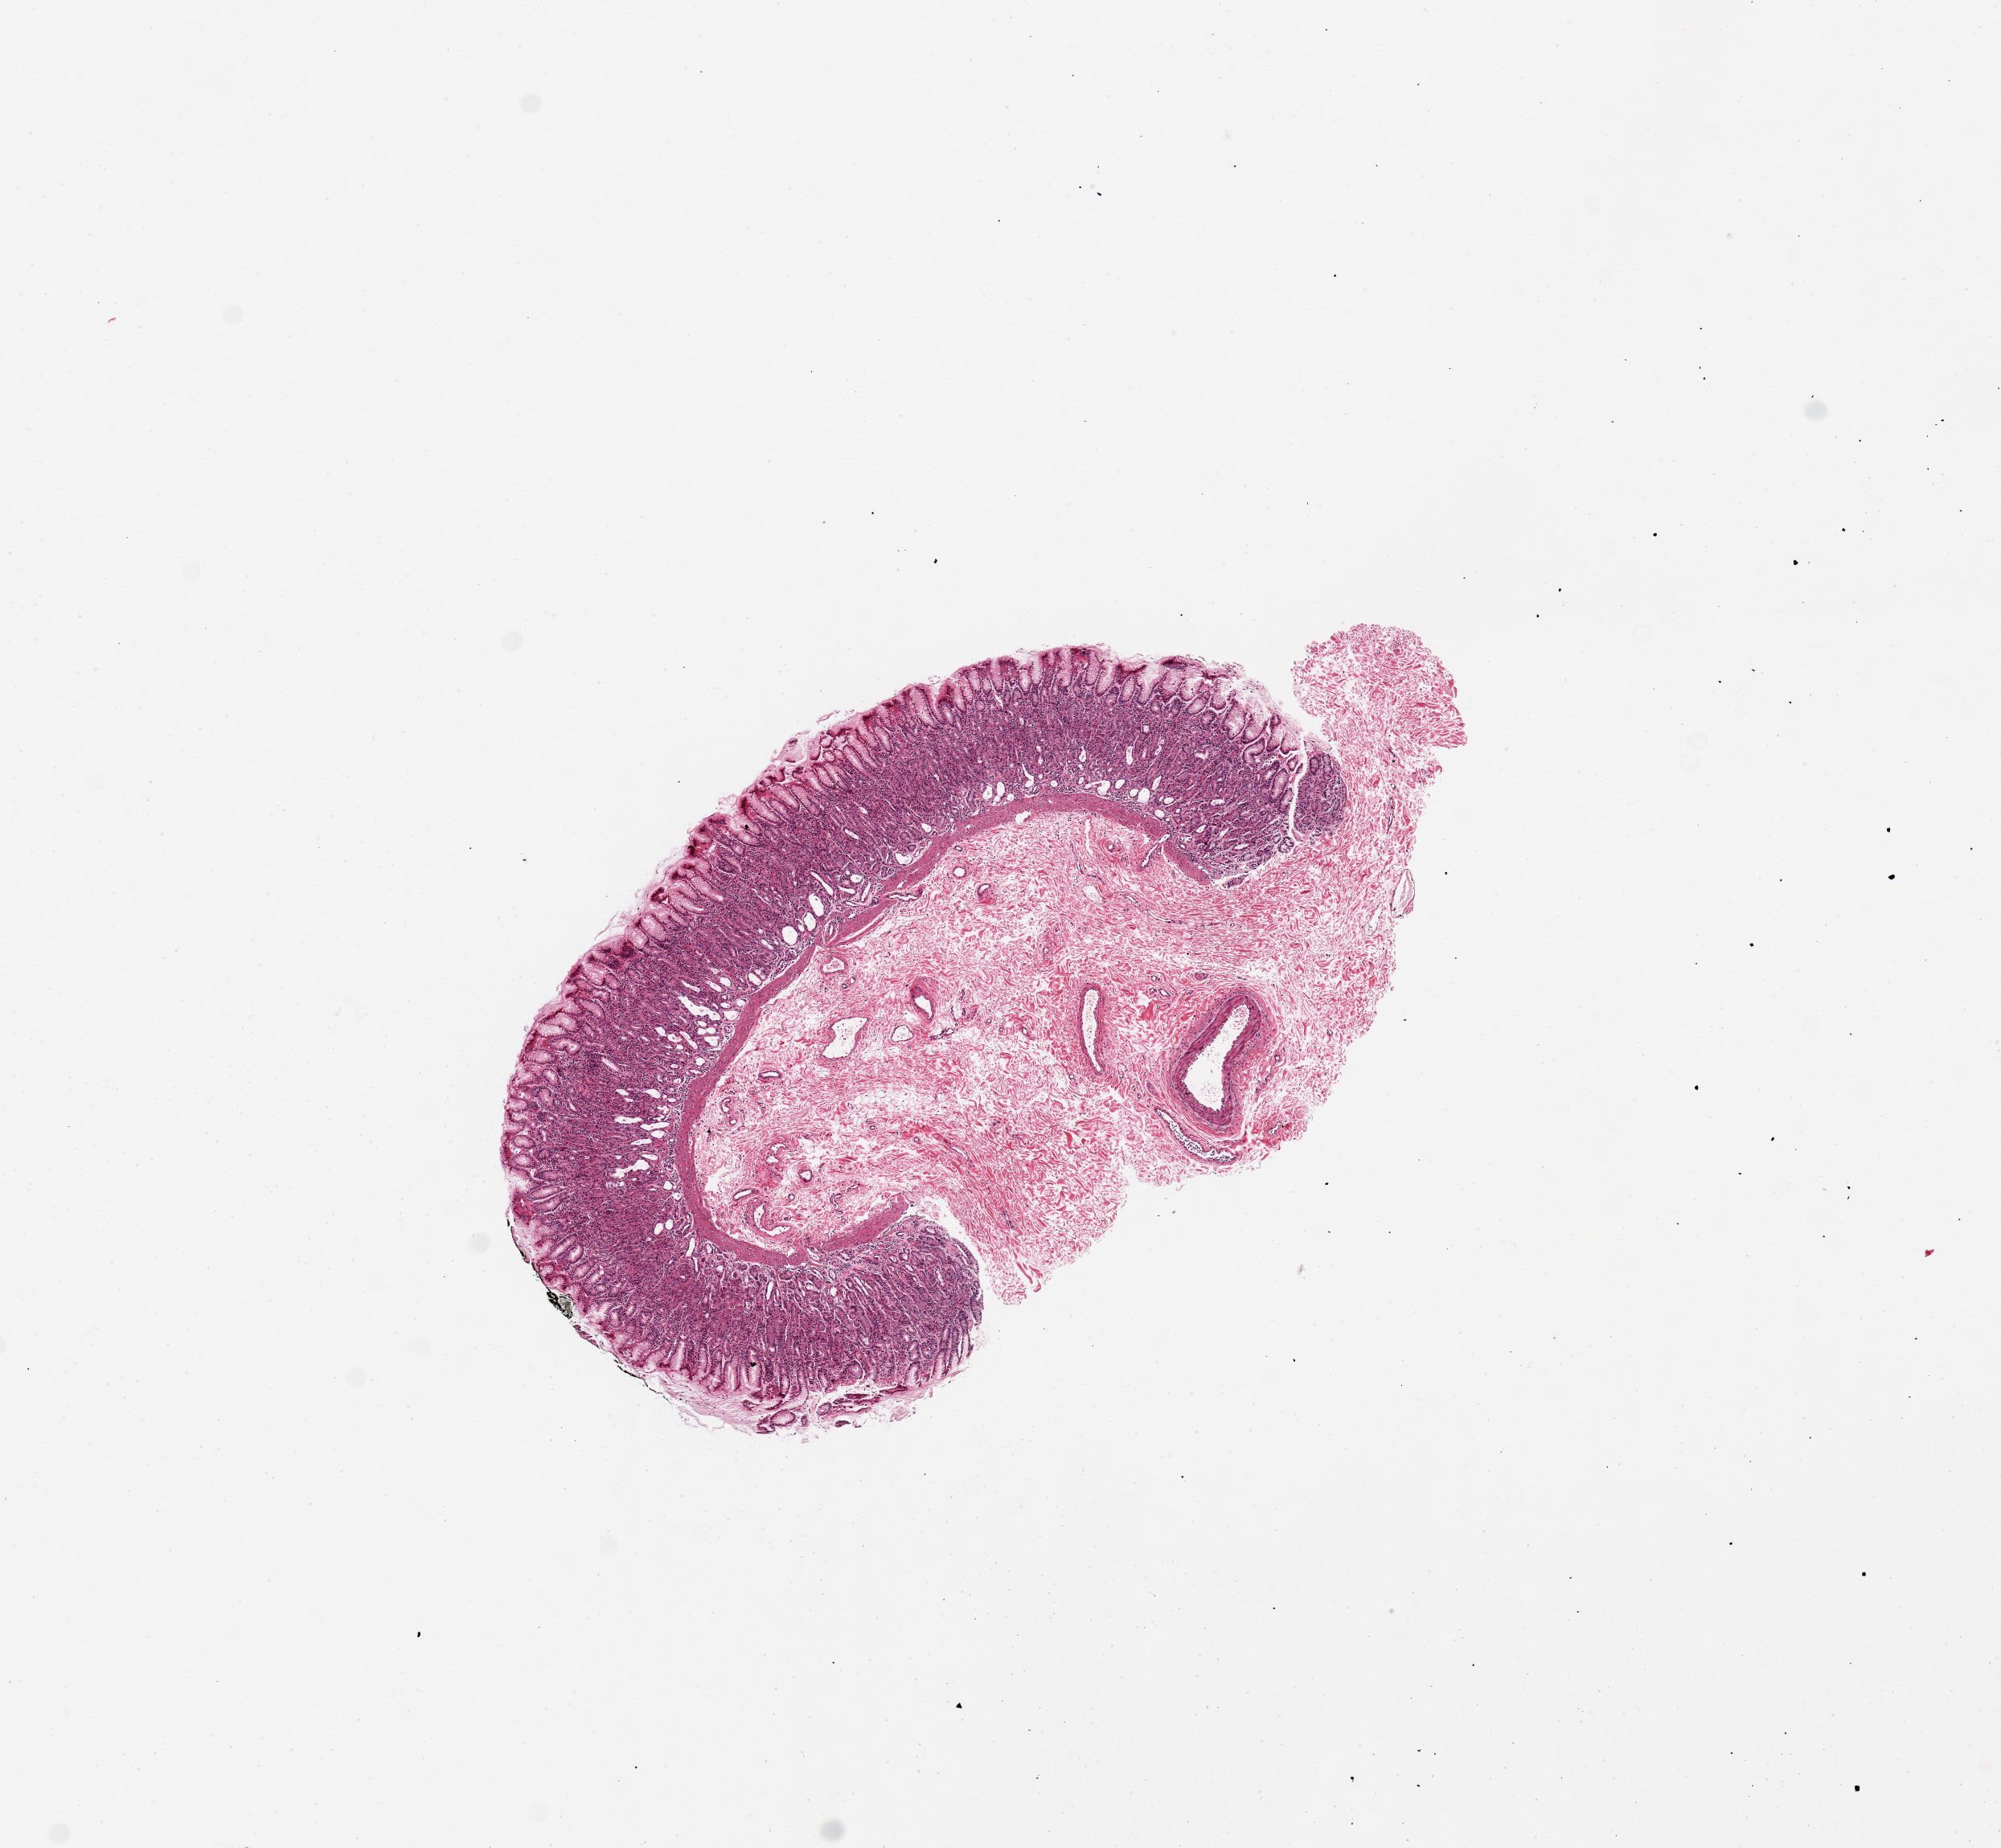
Digitized H&E-stained section — a low-resolution overview of the entire scanned area, about 9.8 x 9.1 mm. PAXgene-fixed paraffin-embedded (PFPE) section. Section of stomach (target tissue). Tissue donor sample. Male donor.
Reviewer comment on this tissue sample: 1 piece. 5x3 mm. Mucosa-submucosa only. Basilar gland dilatation.